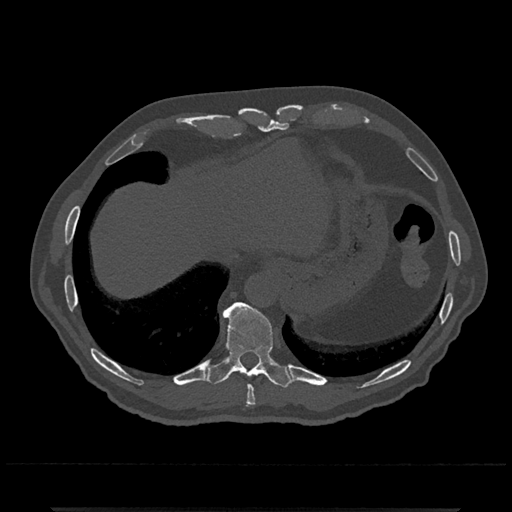
CT including the spine, one axial slice. Position 567 of 797 along the scan axis. Reconstruction kernel Br40s/3. Bone window (W 1800 / L 400 HU). 0.5 mm slice thickness. 512 × 512 image matrix. Male patient, age 67 years. Case-level facts recorded for this patient, not image findings: primary cancer: prostate.
Outlined on this slice (semi-automatically segmented with operator editing):
- T10 vertebra: bounding box [x1, y1, x2, y2] px = [205, 302, 292, 388]
- T9 vertebra: [245, 385, 256, 407]